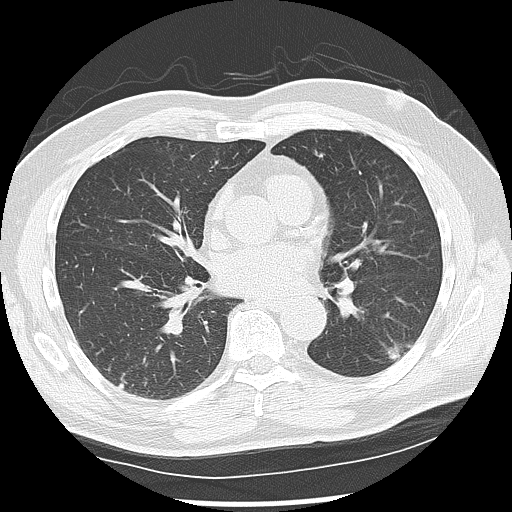
Low-dose screening chest CT, one axial slice; reconstruction kernel LUNG; 120 kVp; lung window (W 1500 / L -600 HU); 2.5 mm slice thickness; 512 × 512 image matrix, field of view 360 × 360 mm.
Annotated regions visible in this slice (manually delineated by an expert):
- lesion 1 (nodule, lower lobe of left lung): bounding box <387,343,412,362> (left, top, right, bottom; pixels)